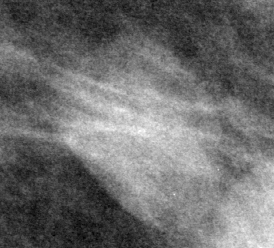
Region of interest cut from a scanned film mammogram (one marked finding), left breast, MLO view.
Finding: mass, shape oval, margins circumscribed; BI-RADS assessment category 3; subtlety rating 5 on a 1 (subtle) to 5 (obvious) scale; pathology result (as recorded, not read from the image): benign.